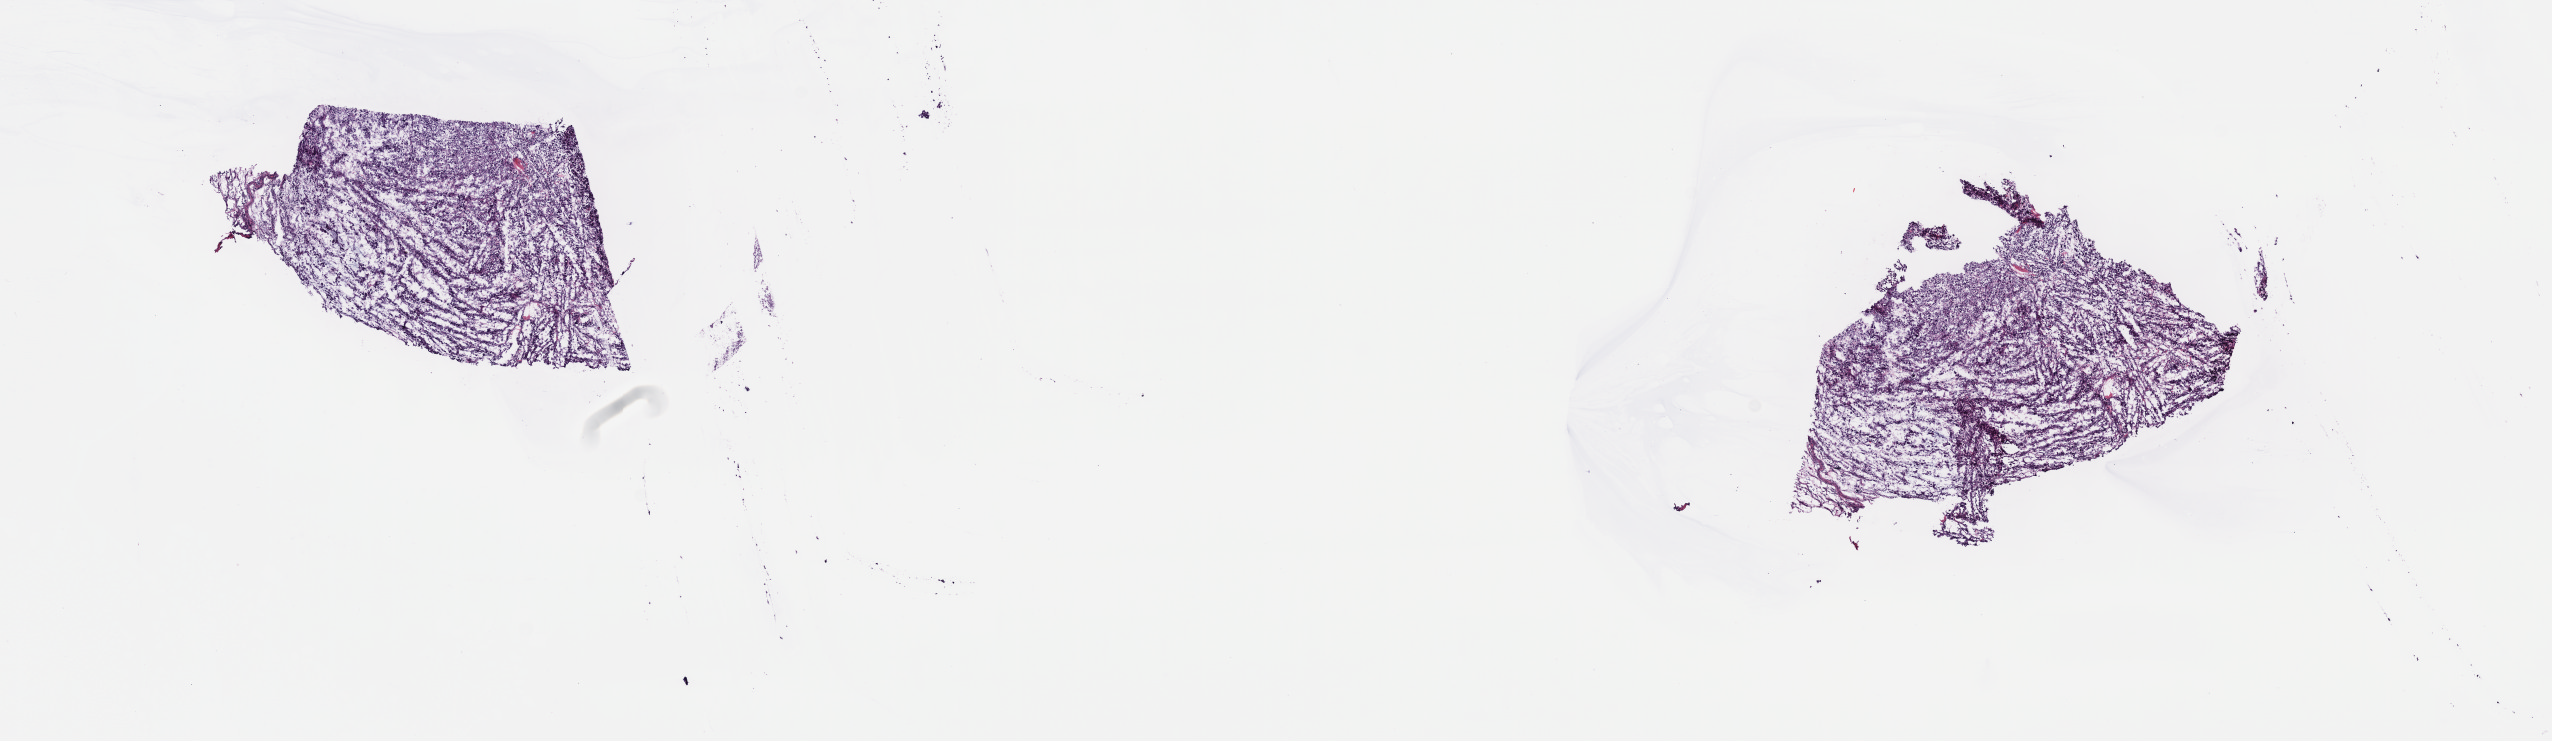
Whole-slide histology image, H&E, shown as a low-resolution overview of the whole scanned area (about 20.6 x 6.0 mm). Frozen section from the top of the tissue portion. Connective, subcutaneous and other soft tissues, primary tumour sample. Male patient; age at initial diagnosis 86 years. Composition of this section per pathologist review: tumour cells 90%, tumour nuclei 95%, normal cells 0%, stromal cells 10%, necrosis 0%. Infiltration values recorded for this section: lymphocyte infiltration 0%, monocyte infiltration 0%, neutrophil infiltration 0%.
• histologic diagnosis: Undifferentiated sarcoma (connective, subcutaneous and other soft tissues of trunk, NOS)